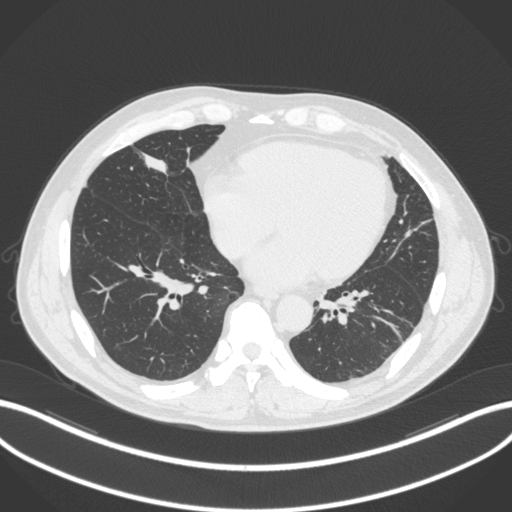
Chest CT, one axial slice. Reconstruction kernel B31f. Lung window (W 1500 / L -600 HU). 1 mm slice thickness. 512 × 512 image matrix, field of view 400 × 400 mm. Patient: male, 59 years. Case-level facts recorded for this patient, not image findings: clinical TNM (as recorded): T2a N1 M0.
Annotated regions visible in this slice (bounding box drawn by a radiologist):
- lung tumour (recorded histology: adenocarcinoma): bounding box (x1, y1, x2, y2) in pixels: (134, 143, 175, 180)